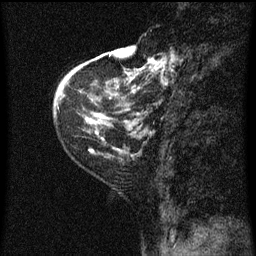
Breast MRI (dynamic contrast-enhanced), one sagittal slice; slice 16 of 60 in the series (ordered by position); dynamic contrast-enhanced series, image 2 of 3 at this slice position (ordered by acquisition); 1.5 T; TE 4.2 ms, TR 8 ms; 2 mm slice thickness; 256 × 256 image matrix, field of view 180 × 180 mm. Patient: female, 48 years.
Outlined on this slice (semi-automatic segmentation, software-assisted and operator-edited):
- analysis volume of interest (the breast-tissue region the enhancement analysis was run in; not a lesion): bounding box (x1, y1, x2, y2) in pixels: (128, 54, 175, 125)
- tumour enhancement mask (voxels above the 70 % enhancement threshold inside the analysis volume of interest): (128, 54, 175, 121)